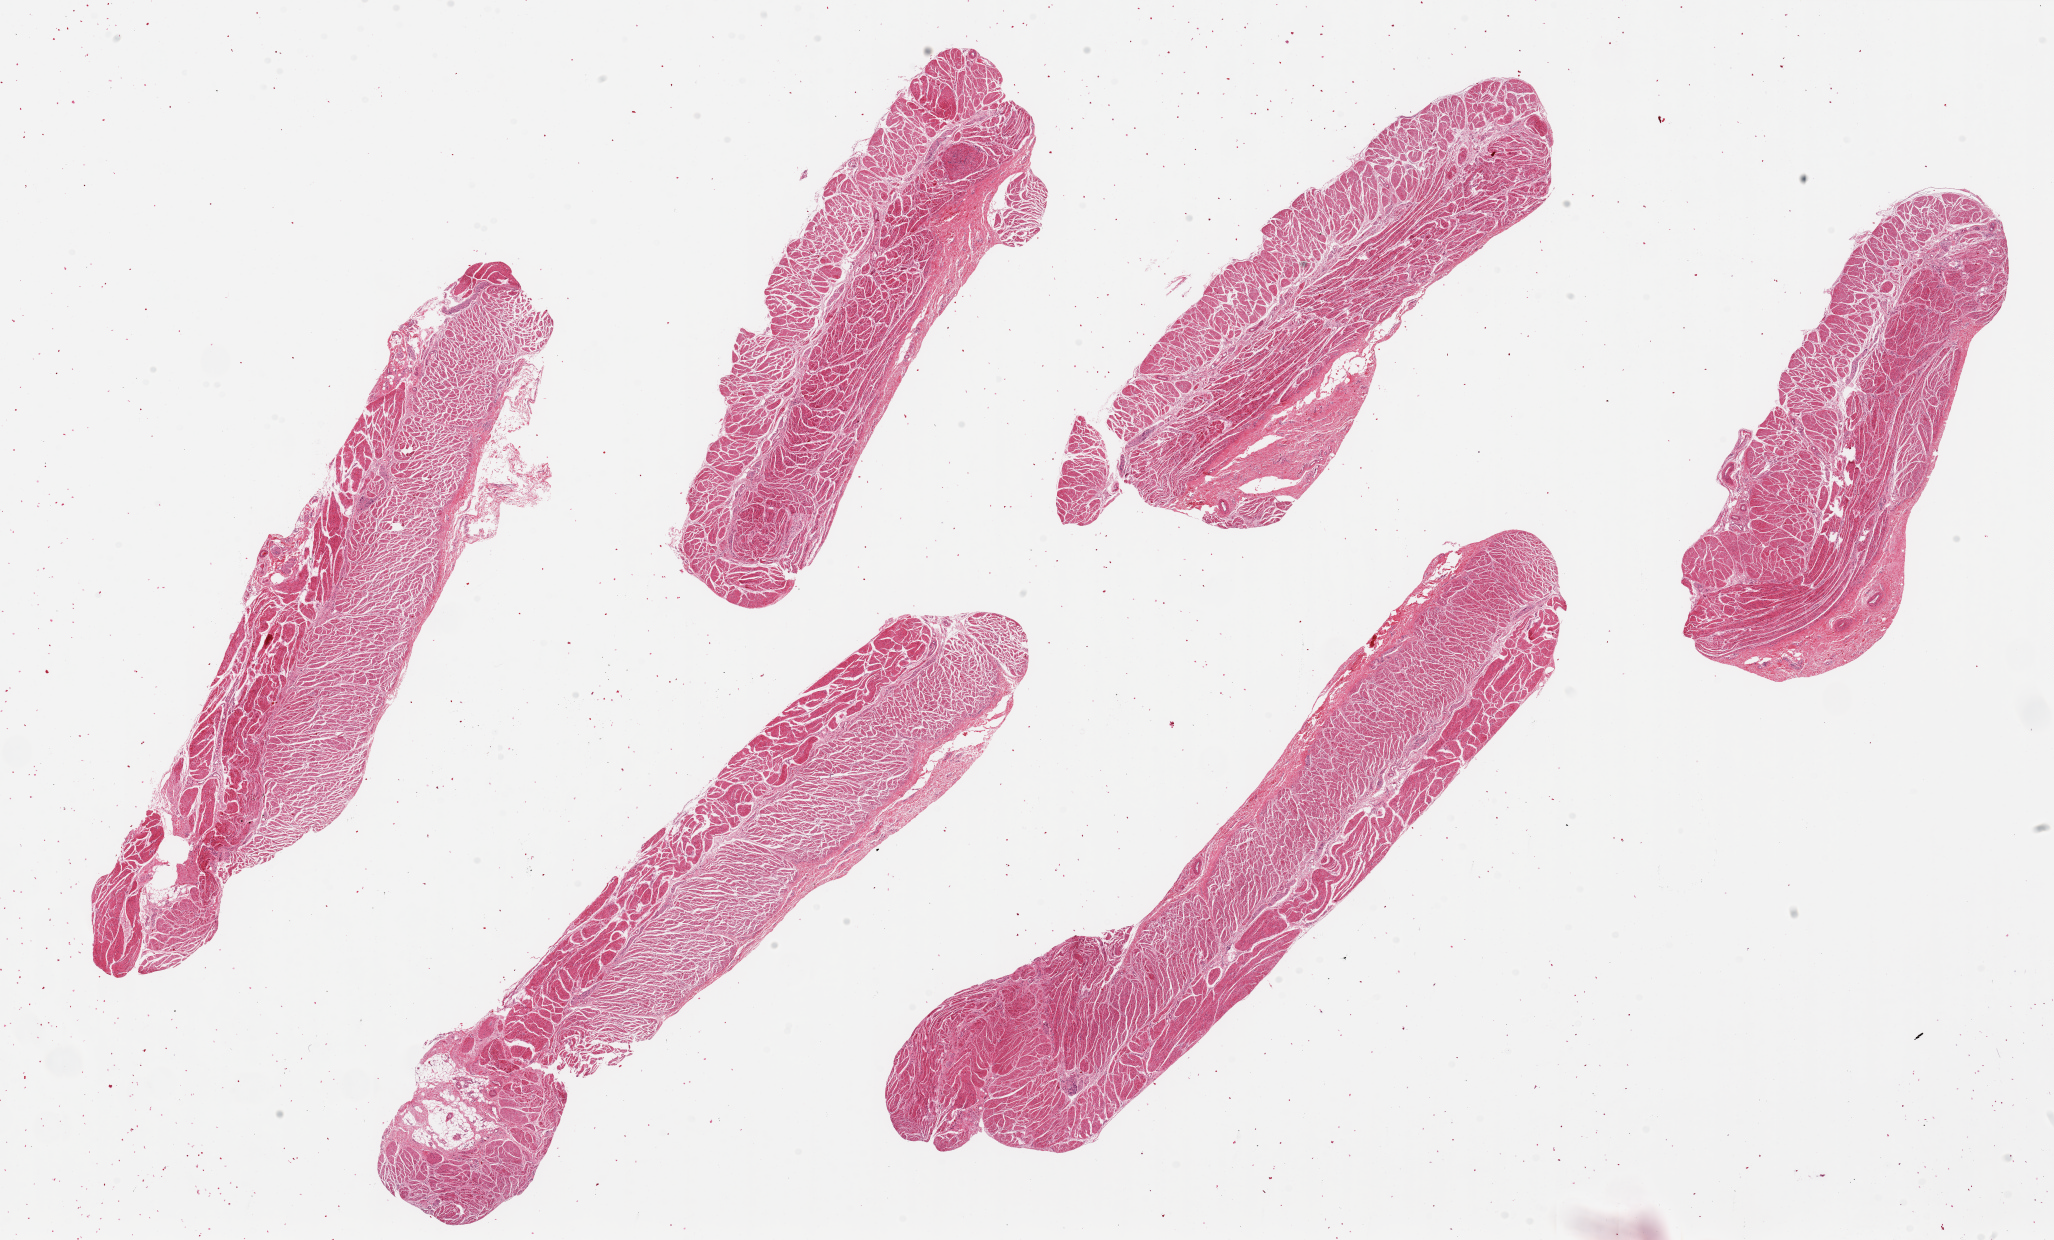
H&E whole-slide image, brightfield — whole scanned area (about 32.5 x 19.6 mm) shown as a low-resolution overview, PAXgene-fixed paraffin-embedded (PFPE) section, target tissue: gastroesophageal junction, tissue donor sample. Male donor.
• review note (as recorded): 6 pieces ~11x3mm, all muscularis; good specimens